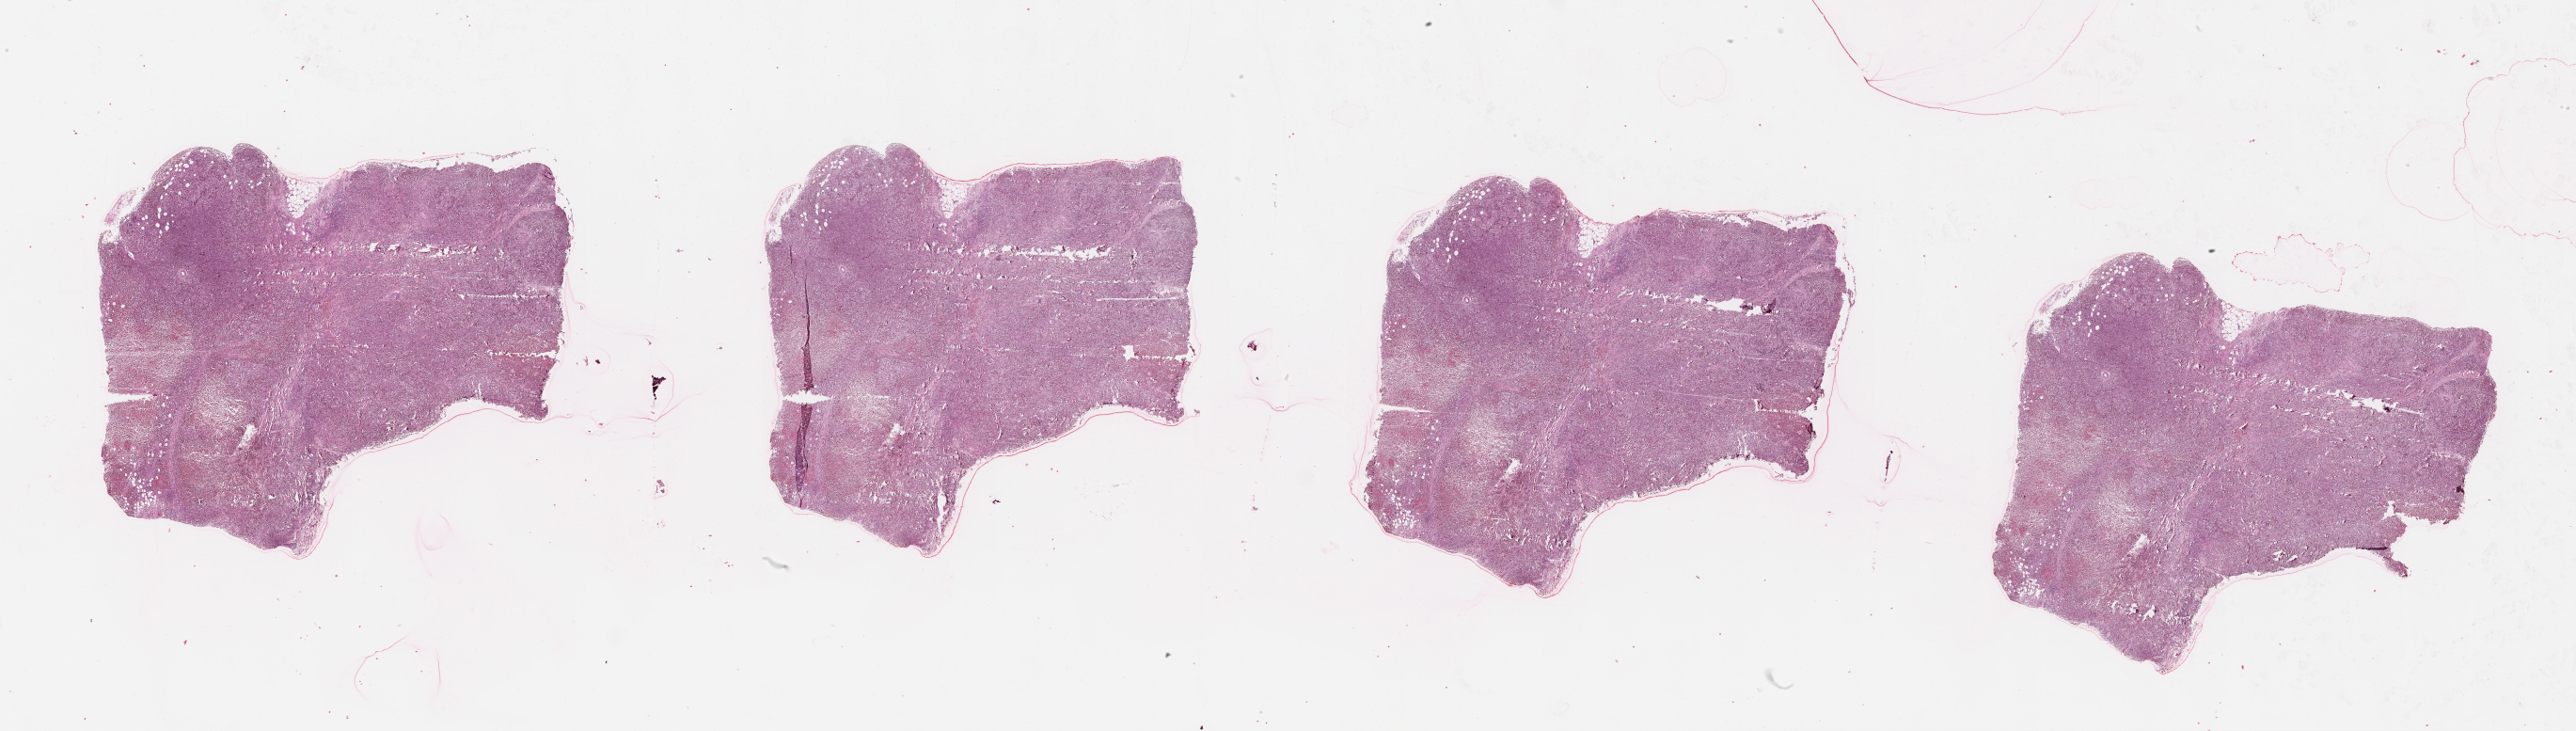
Digitized H&E tissue section (whole slide) — low-resolution overview of the scanned area, about 44.1 x 12.5 mm (acquisition: 20x scan), tumour tissue sample, sampled site: skin. Patient: female, age 76 years. Composition of this section per pathologist review: tumour nuclei 80%, necrosis 10%.
- AJCC pathologic stage: IIC
- diagnosis: Malignant melanoma, NOS